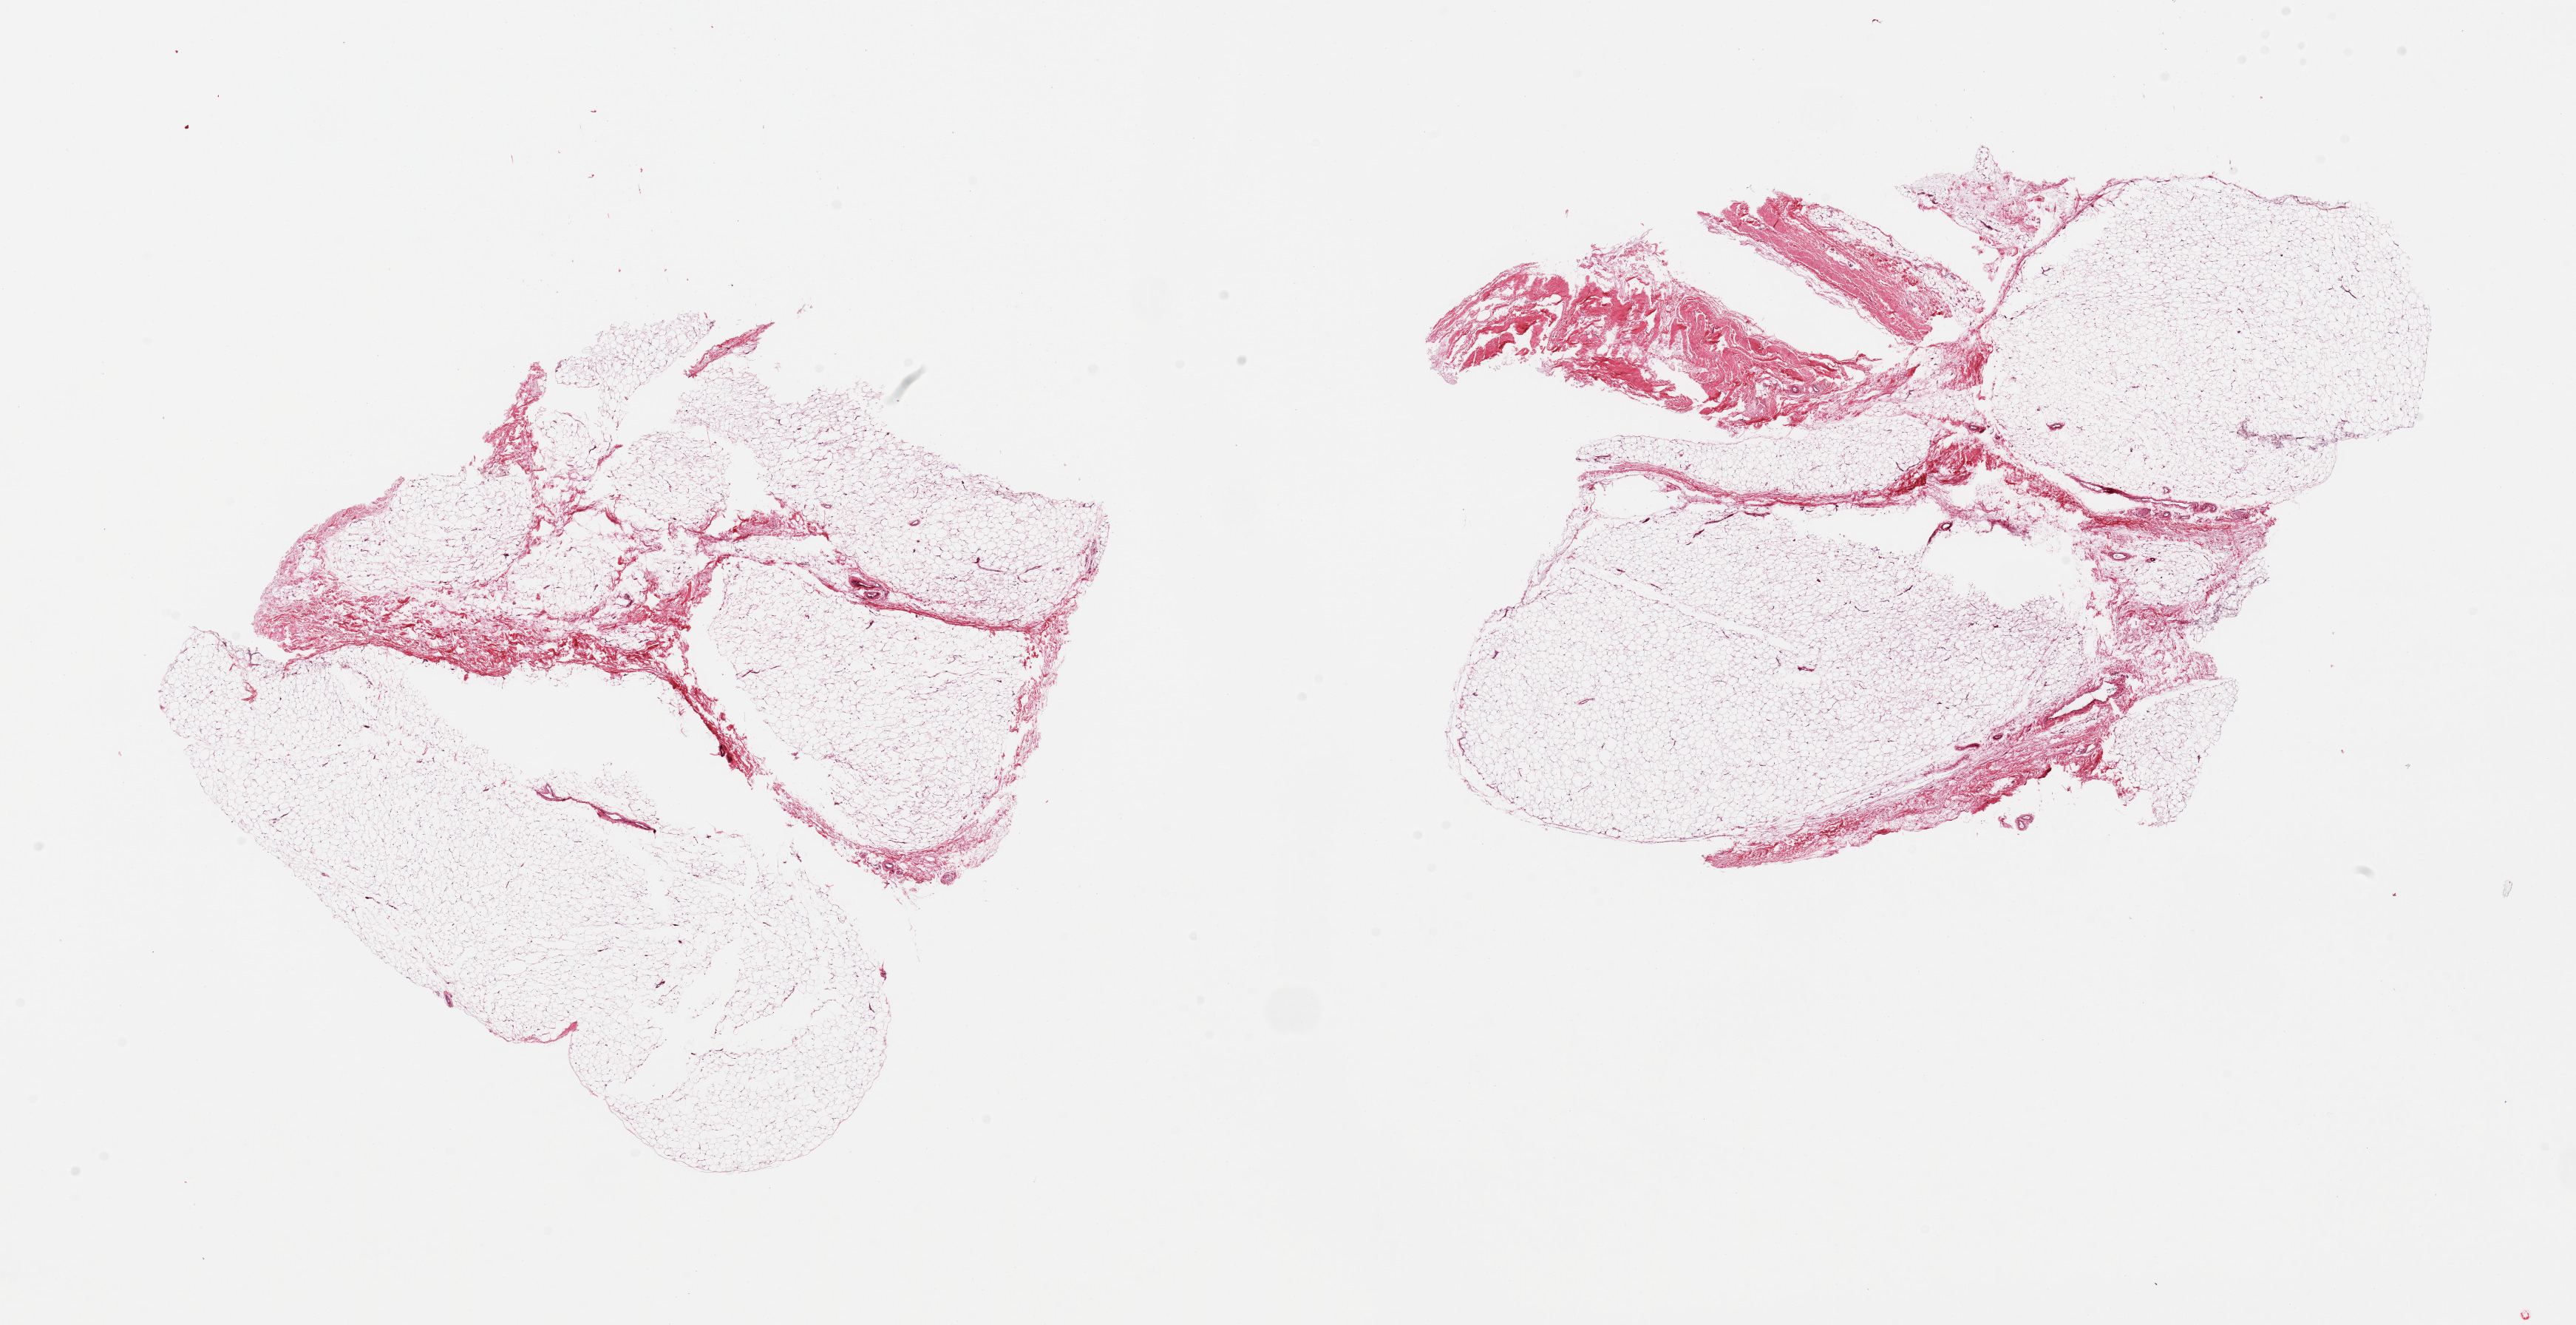
Digitized hematoxylin and eosin (H&E)-stained section, a low-resolution overview of the entire scanned area, about 27.6 x 14.2 mm, PAXgene-fixed, paraffin-embedded tissue, target tissue: adipose tissue, donor tissue sample. Donor sex: male.
Pathologist's review note for this sample: 2 pieces; ~20% fascia.